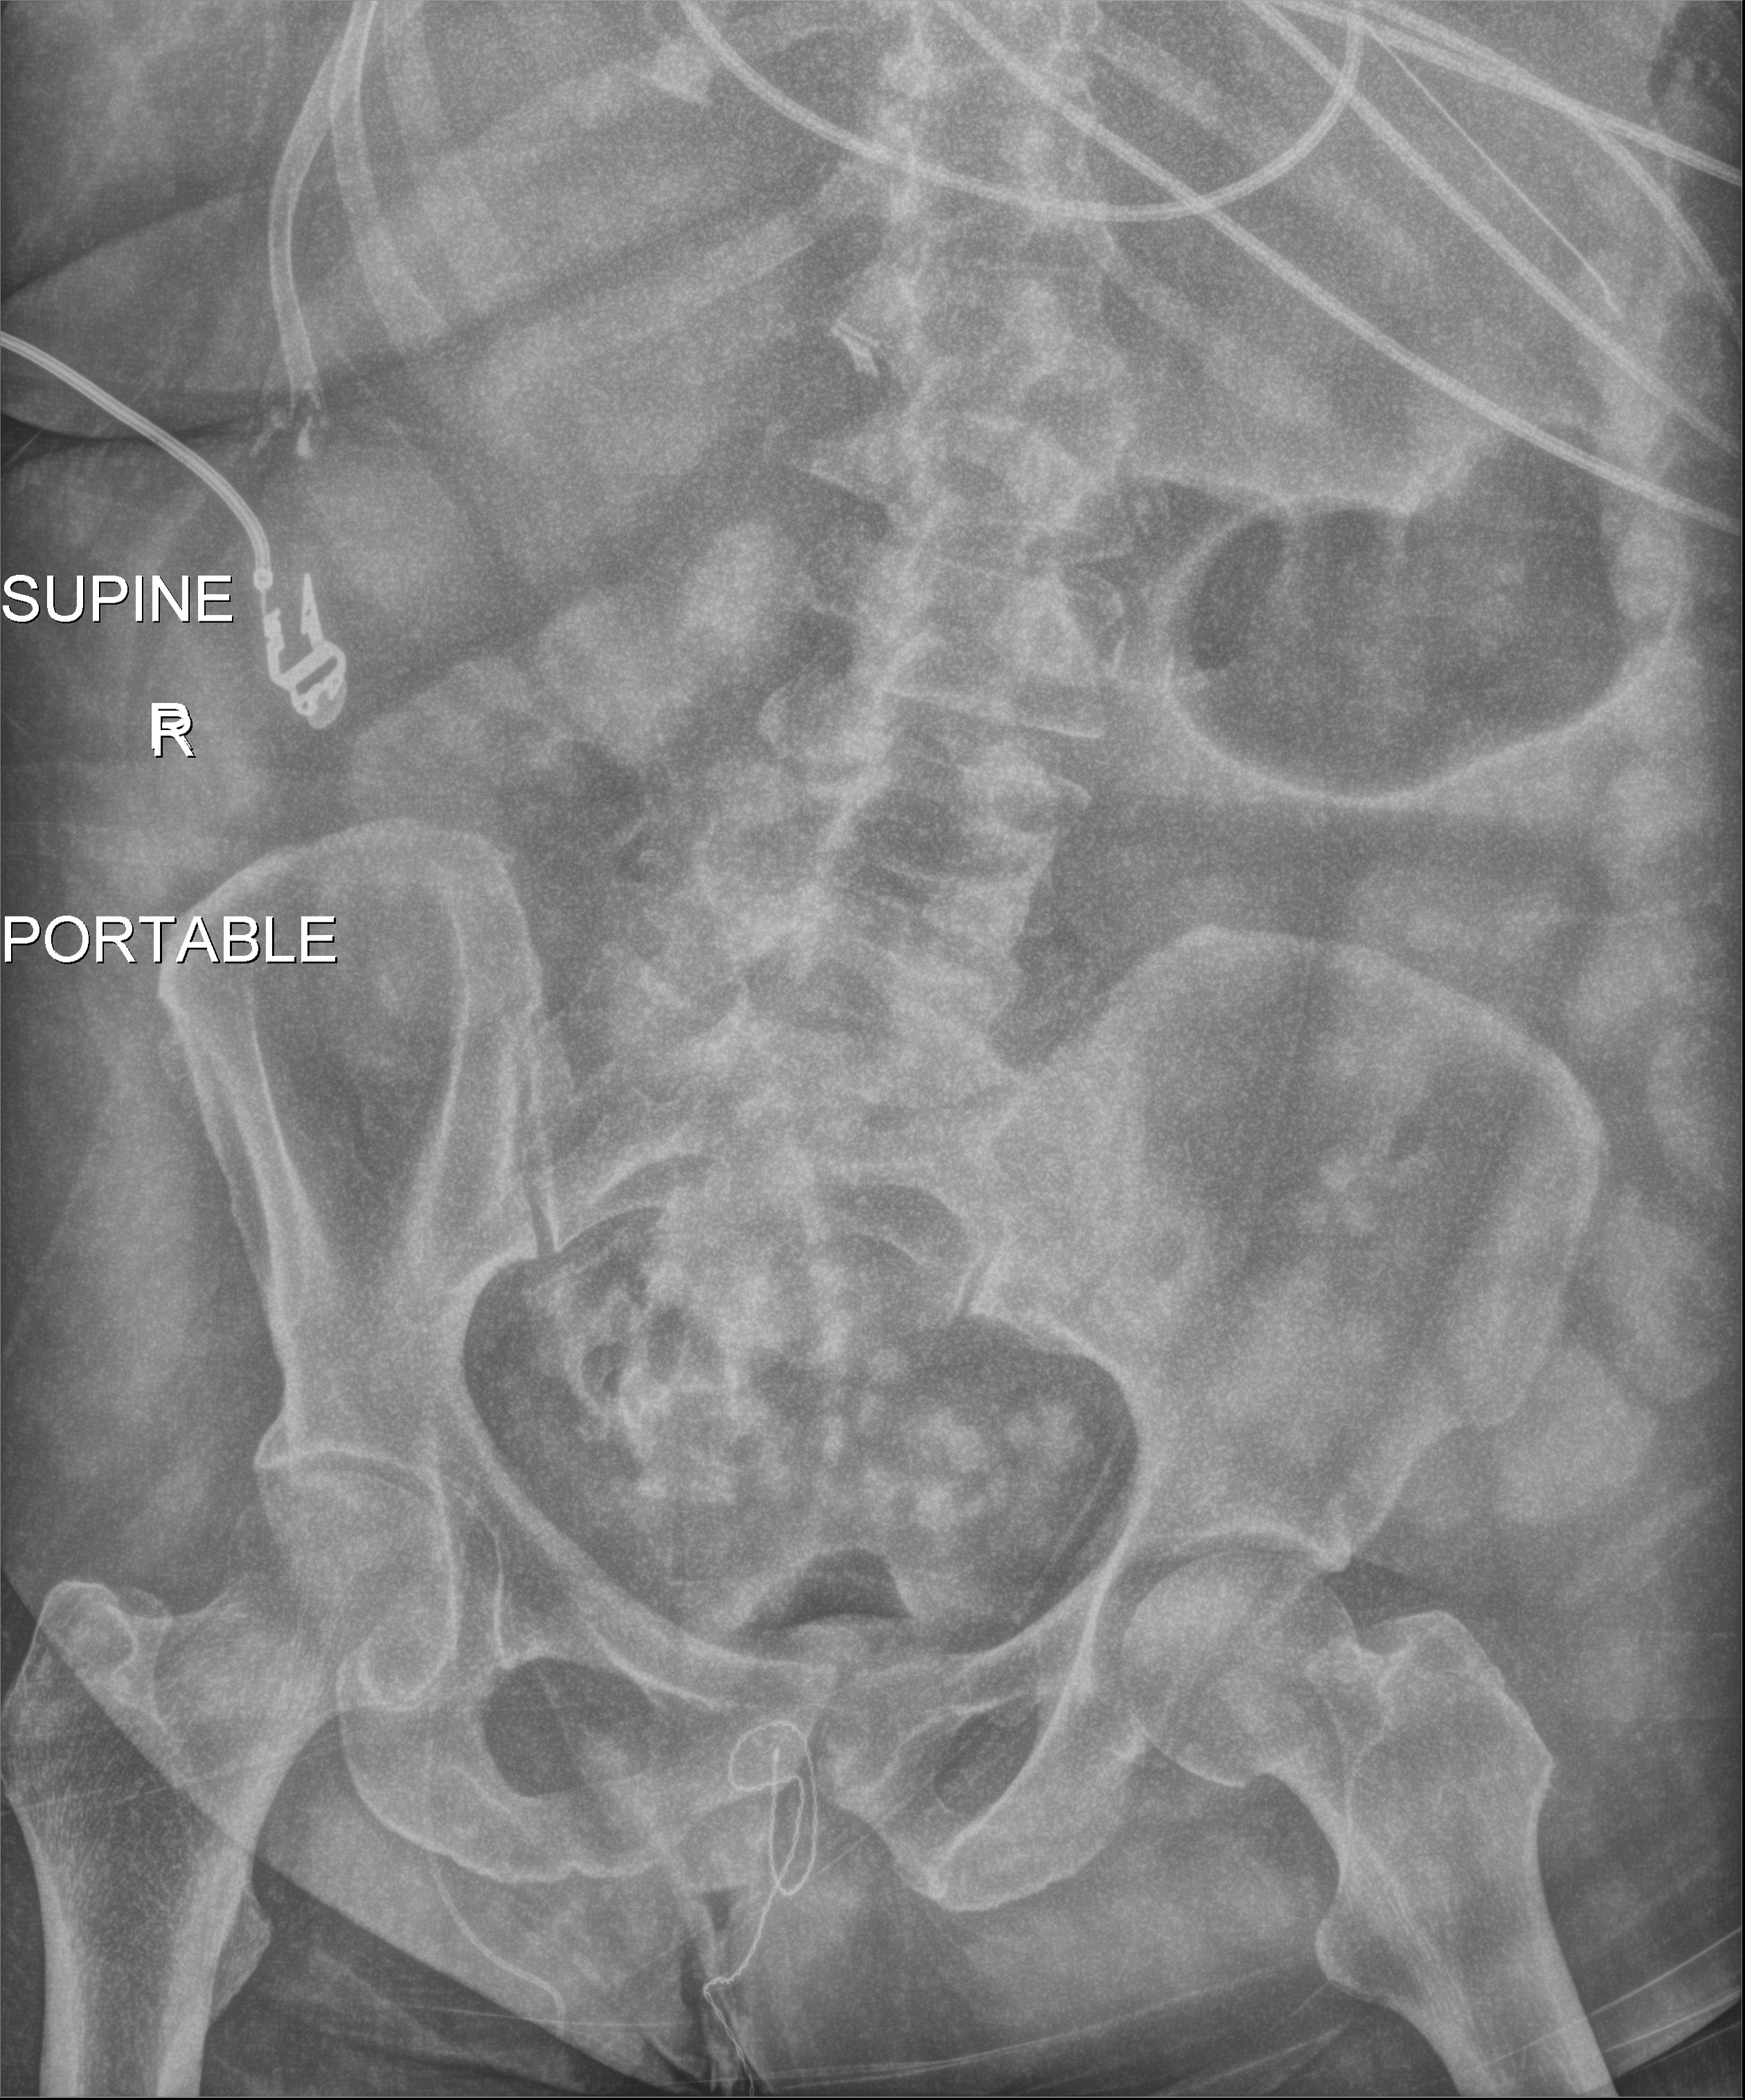
Bedside abdomen radiograph (digital radiography); anteroposterior (AP) projection. Female patient hospitalised with COVID-19, age 60–74 years.
From the hospital-stay record, not from the radiograph (when in the stay this image was taken is not recorded): chronic kidney disease (admission record): no; admitted to intensive care during this hospital stay: yes; mechanically ventilated during this hospital stay: yes.